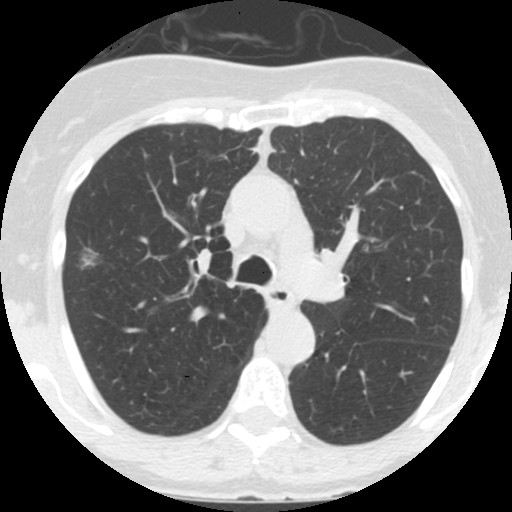
Low-dose screening chest CT, one axial slice. Position 97 of 146 along the scan axis. Reconstruction kernel STANDARD. 120 kVp. Lung window (W 1500 / L -600 HU). 2.5 mm slice thickness. 512 × 512 image matrix.
Annotated regions visible in this slice (manually delineated by an expert):
- lesion 1 (tumor, upper lobe of right lung): box from (x=79, y=248) to (x=98, y=270) px